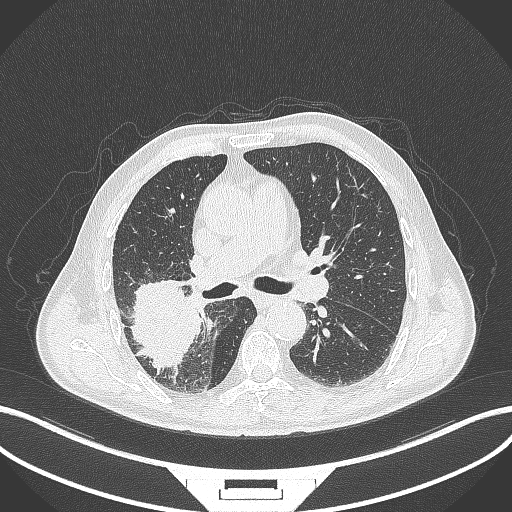
Chest CT, one axial slice; position 244 of 429 along the scan axis; lung window (W 1500 / L -600 HU); 1 mm slice thickness; 512 × 512 image matrix, field of view 400 × 400 mm. Male patient, age 72 years. From the clinical record (not read from this slice): clinical TNM (as recorded): T3 N2 M0.
Outlined on this slice (bounding box drawn by a radiologist):
- lung tumour (recorded histology: adenocarcinoma): box from (x=122, y=271) to (x=205, y=375) px